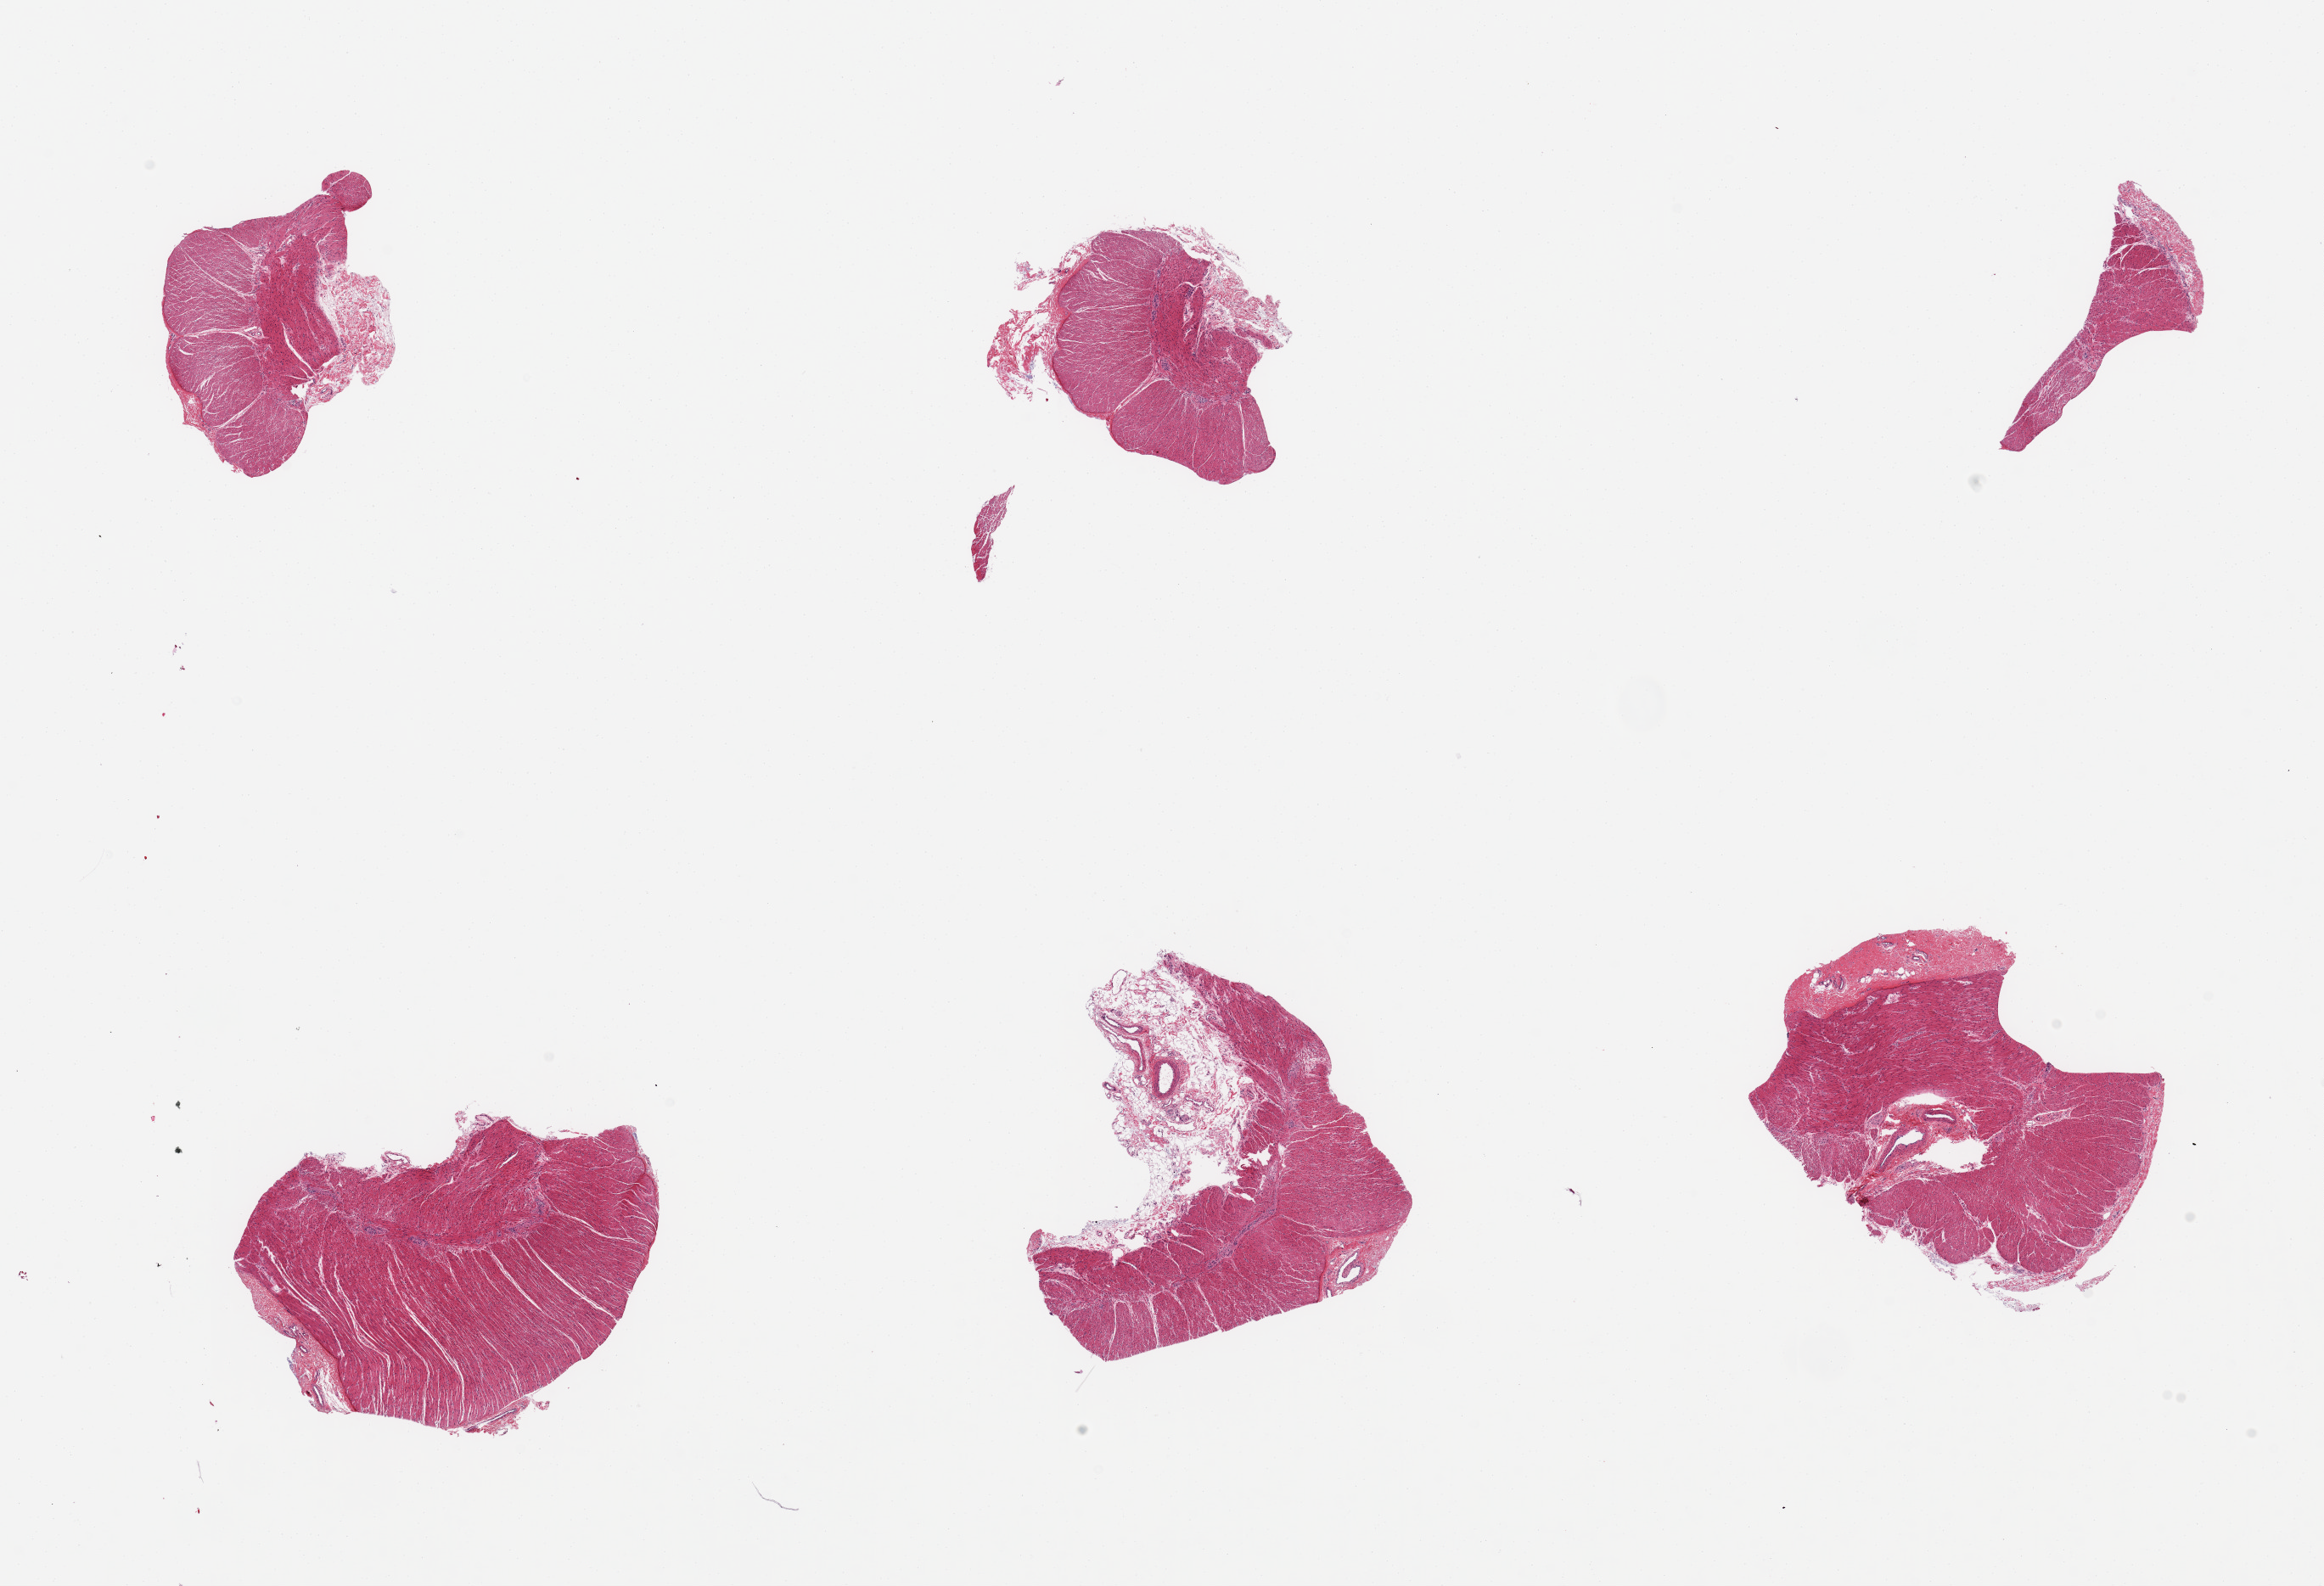
Haematoxylin and eosin whole-slide image, brightfield, shown as a low-resolution overview of the whole scanned area (about 21.7 x 14.8 mm, acquisition: 20x scan). PAXgene-fixed, paraffin-embedded tissue. Section of sigmoid colon (target tissue). Donor tissue sample.
Review note (as recorded): 6 pieces; muscularis with varying amounts of fibrous and fatty tissue up to 30%.